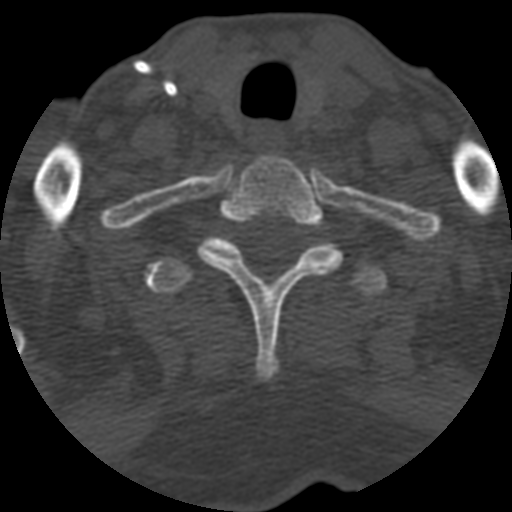
CT including the spine, one axial slice; slice 515 of 708 in the series (ordered by position); reconstruction kernel STANDARD; one of 3 acquisitions stored at this slice position; bone window (W 1800 / L 400 HU); 1.25 mm slice thickness; 512 × 512 image matrix. Patient age 55 years. From the clinical record (not read from this slice): primary cancer: colon; vertebrae with lytic lesions (as recorded): T12, L1, L5.
Annotated regions visible in this slice (semi-automatically segmented with operator editing):
- T1 vertebra: bounding box [x1, y1, x2, y2] px = [198, 155, 344, 377]
- T2 vertebra: [144, 235, 388, 298]